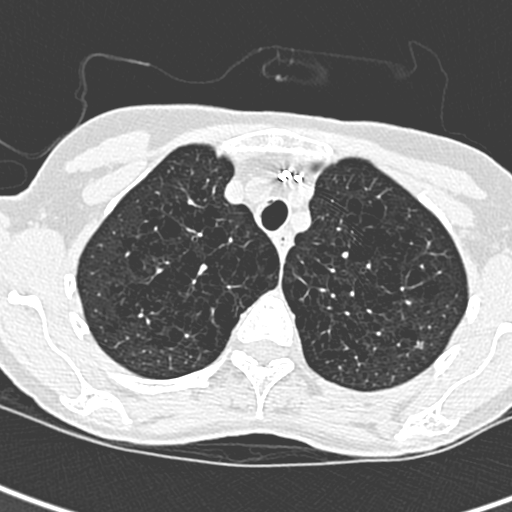
Chest CT (low-dose screening protocol), one axial image. Baseline screening round. Lung window (W 1500 / L -600 HU). 1.3 mm slice thickness. Lung (sharp) reconstruction kernel (D). Slice 52 of 259 in the series. Female, age 71 years at enrolment.
- Expert reader's lesion annotation, bounding box <398,326,436,364> (left, top, right, bottom; pixels).
- No non-calcified nodule or mass ≥4 mm was recorded by the screening reader at this exam.
- Official screen result: negative screen, no significant abnormalities.
- Participant outcome: lung cancer diagnosed 975 days after this screen — adenocarcinoma, NOS, left upper lobe, moderately differentiated (G2), stage IA (AJCC 6th edition), 12 mm at pathology.